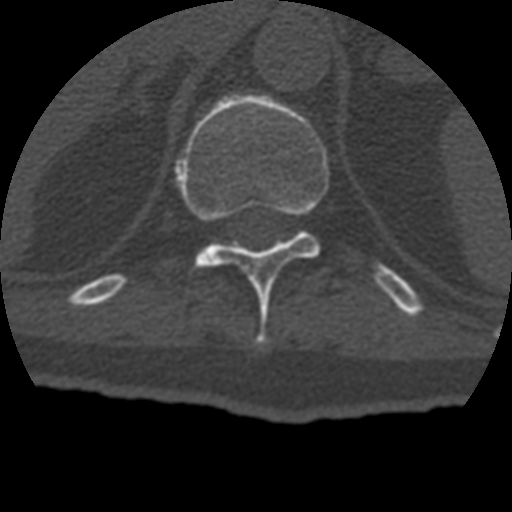
CT including the spine, one axial slice; slice 193 of 399 in the series (ordered by position); bone window (W 1800 / L 400 HU); 1.25 mm slice thickness; 512 × 512 image matrix, field of view 160 × 160 mm. Patient age 69 years. Case-level facts recorded for this patient, not image findings: primary cancer: prostate.
Structures marked on this image (semi-automatically segmented with operator editing):
- T11 vertebra: box from (x=175, y=94) to (x=330, y=345) px